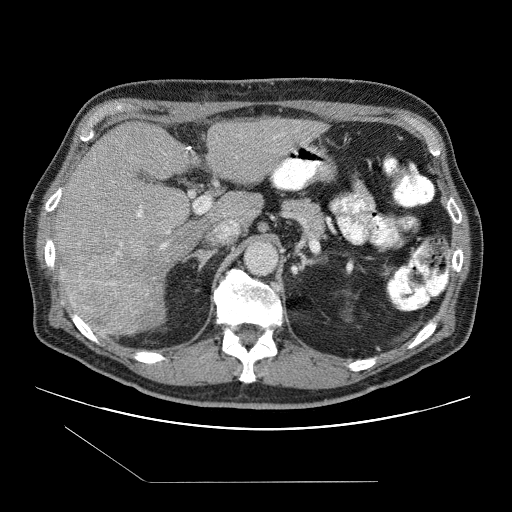
Contrast-enhanced abdominal CT (liver protocol), one axial slice. Slice 58 of 109 in the series (ordered by position). Reconstruction kernel STANDARD. 120 kVp. One of 2 acquisitions stored at this slice position. Soft-tissue window (W 400 / L 40 HU). 2.5 mm slice thickness. 512 × 512 image matrix. From the clinical record (not read from this slice): diagnosis: hepatocellular carcinoma (patient treated with transarterial chemoembolisation; whether this scan precedes or follows treatment is not stated here); TNM stage (as recorded): Stage-IIIB; Child-Pugh class: A; tumour nodularity: multinodular.
Annotated regions visible in this slice (semi-automatic segmentation, software-assisted and operator-edited):
- liver parenchyma outside the tumour (the mass and vessels are separate outlines, so this box may not span the whole liver): box from (x=54, y=118) to (x=324, y=334) px
- mass: (x=66, y=249)–(x=155, y=335)
- liver vessels: (x=137, y=137)–(x=276, y=248)